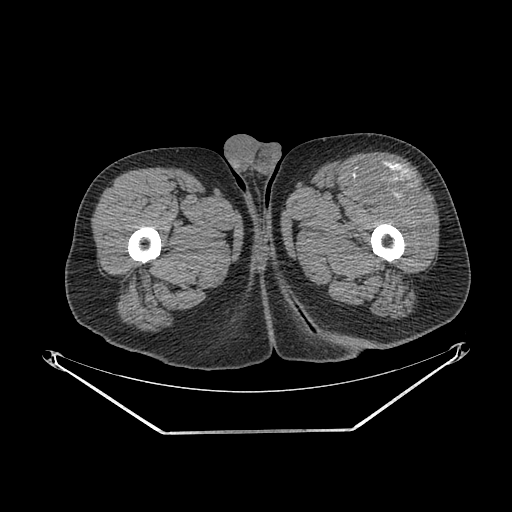
CT of an extremity soft-tissue mass (from a PET/CT study), one axial slice. Slice 253 of 267 in the series (ordered by position). Soft-tissue window (W 400 / L 40 HU). 512 × 512 image matrix. Male patient. Case-level facts recorded for this patient, not image findings: histological type: extraskeletal osteosarcoma; grade: high; site of the primary tumour: thigh.
Outlined on this slice (expert contour drawn on MRI and transferred to this co-registered scan by the dataset authors):
- gross tumour volume (mass): bounding box (x1, y1, x2, y2) in pixels: (363, 169, 419, 200)